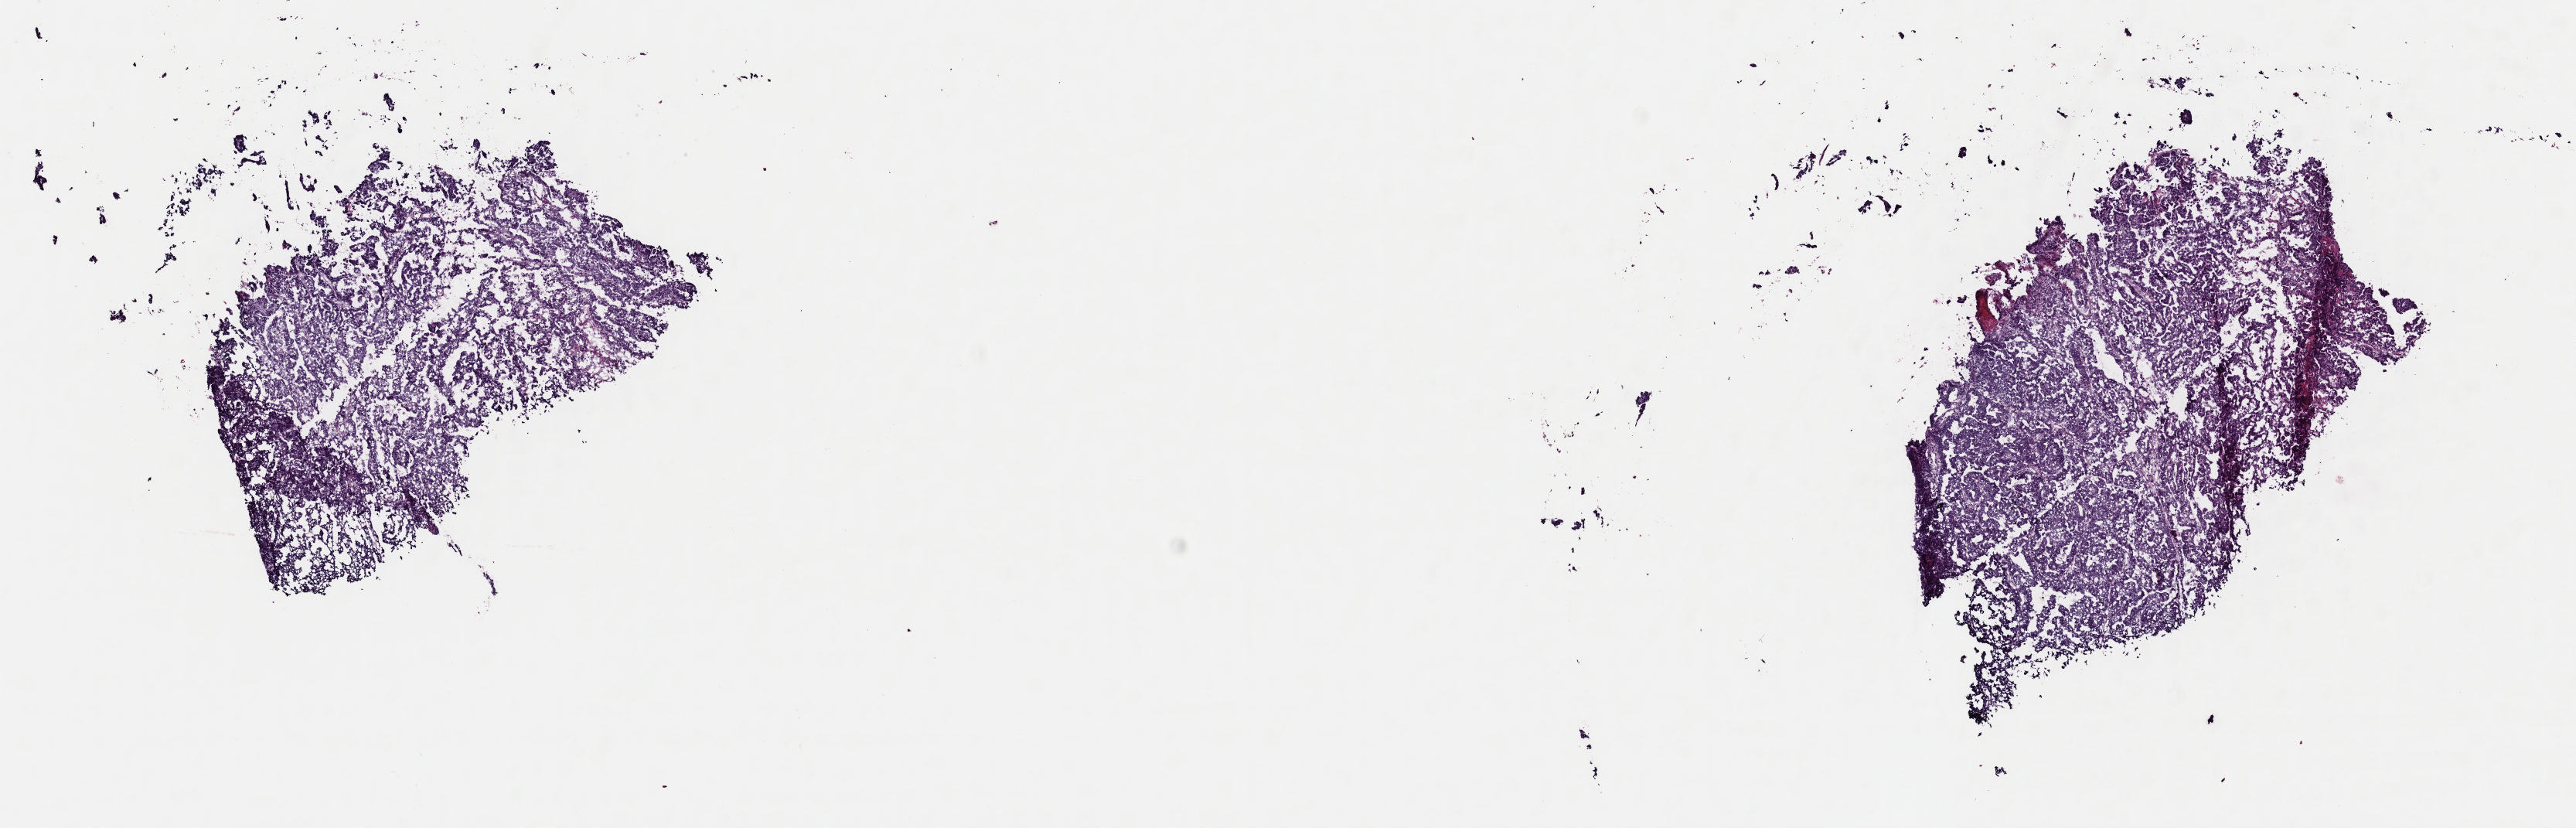
Digitized H&E-stained tissue section (whole slide), shown as a low-resolution overview of the whole scanned area (about 13.2 x 4.2 mm, from a 40x scan); frozen section from the top of the tissue portion; uterus, primary tumour sample. Patient: female, age at initial diagnosis 60 years. Slide review estimates, as recorded: tumour cells 95%, tumour nuclei 90%.
Diagnosis: Serous cystadenocarcinoma, NOS (endometrium).